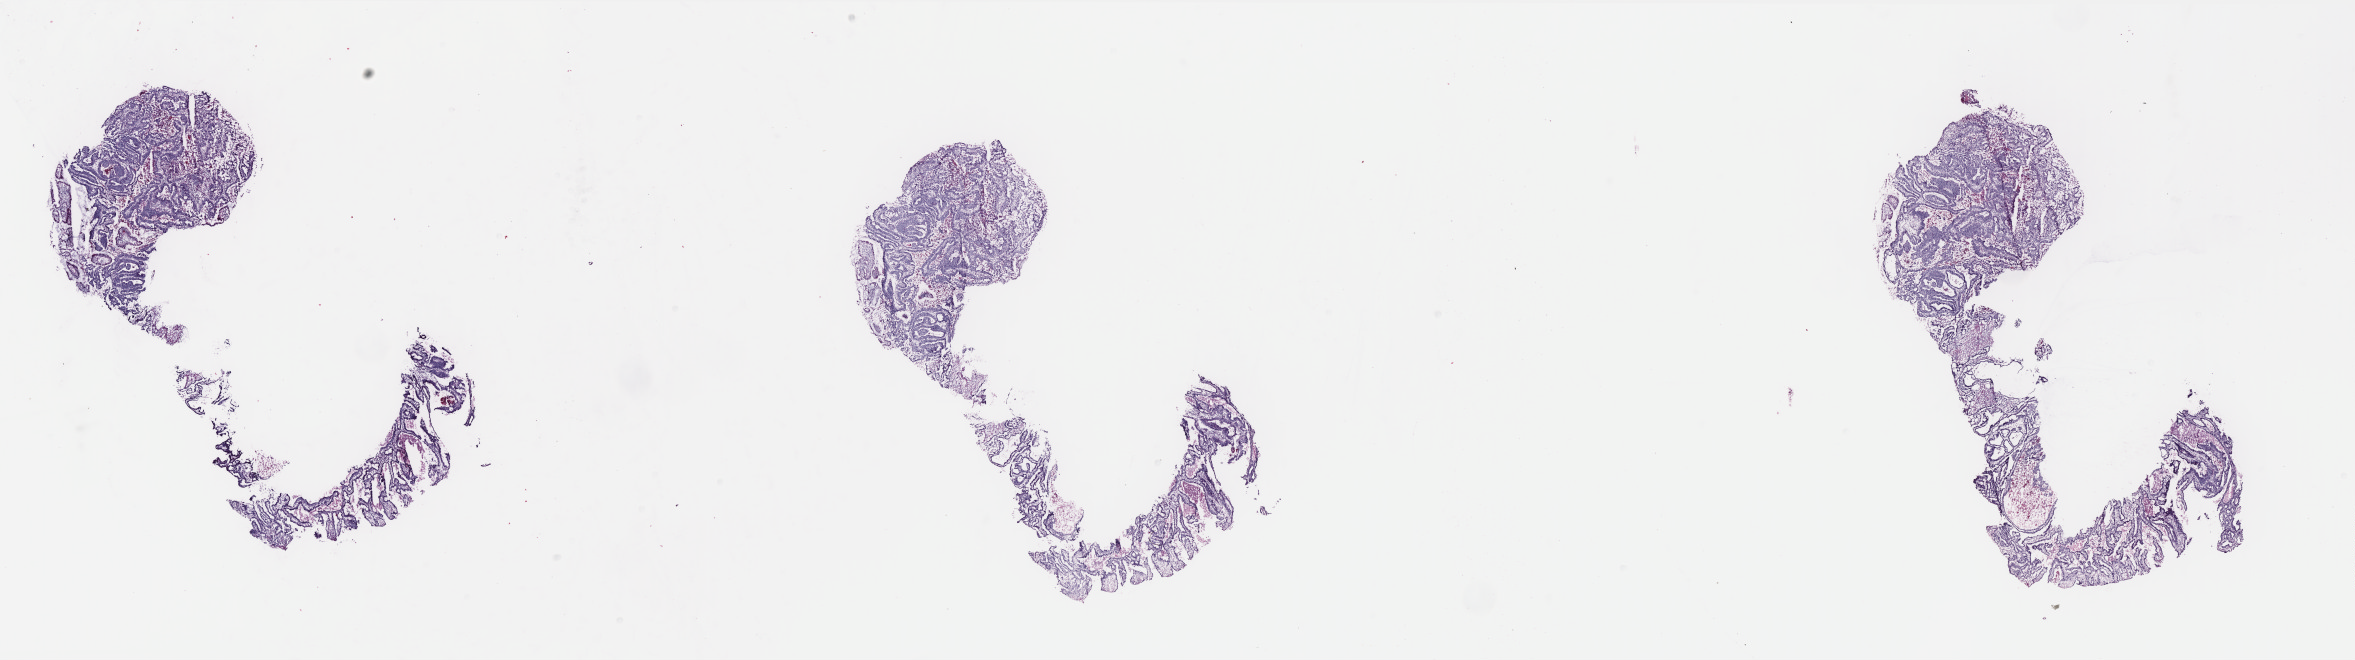
Hematoxylin and eosin (H&E) stained whole-slide image — whole scanned area (about 37.8 x 10.6 mm) shown as a low-resolution overview; frozen section; colon, primary tumour sample. Male, age 66 years at initial diagnosis. Slide review estimates, as recorded: tumour cells 95%, tumour nuclei 85%, normal cells 0%, stromal cells 0%, necrosis 5%. Infiltration values recorded for this section: lymphocyte infiltration 3%, monocyte infiltration 2%, neutrophil infiltration 1%.
AJCC pathologic stage: IIA (6th edition). Diagnosis: Adenocarcinoma, NOS (transverse colon). Lymph nodes positive (case pathology): 0 of 32 examined.